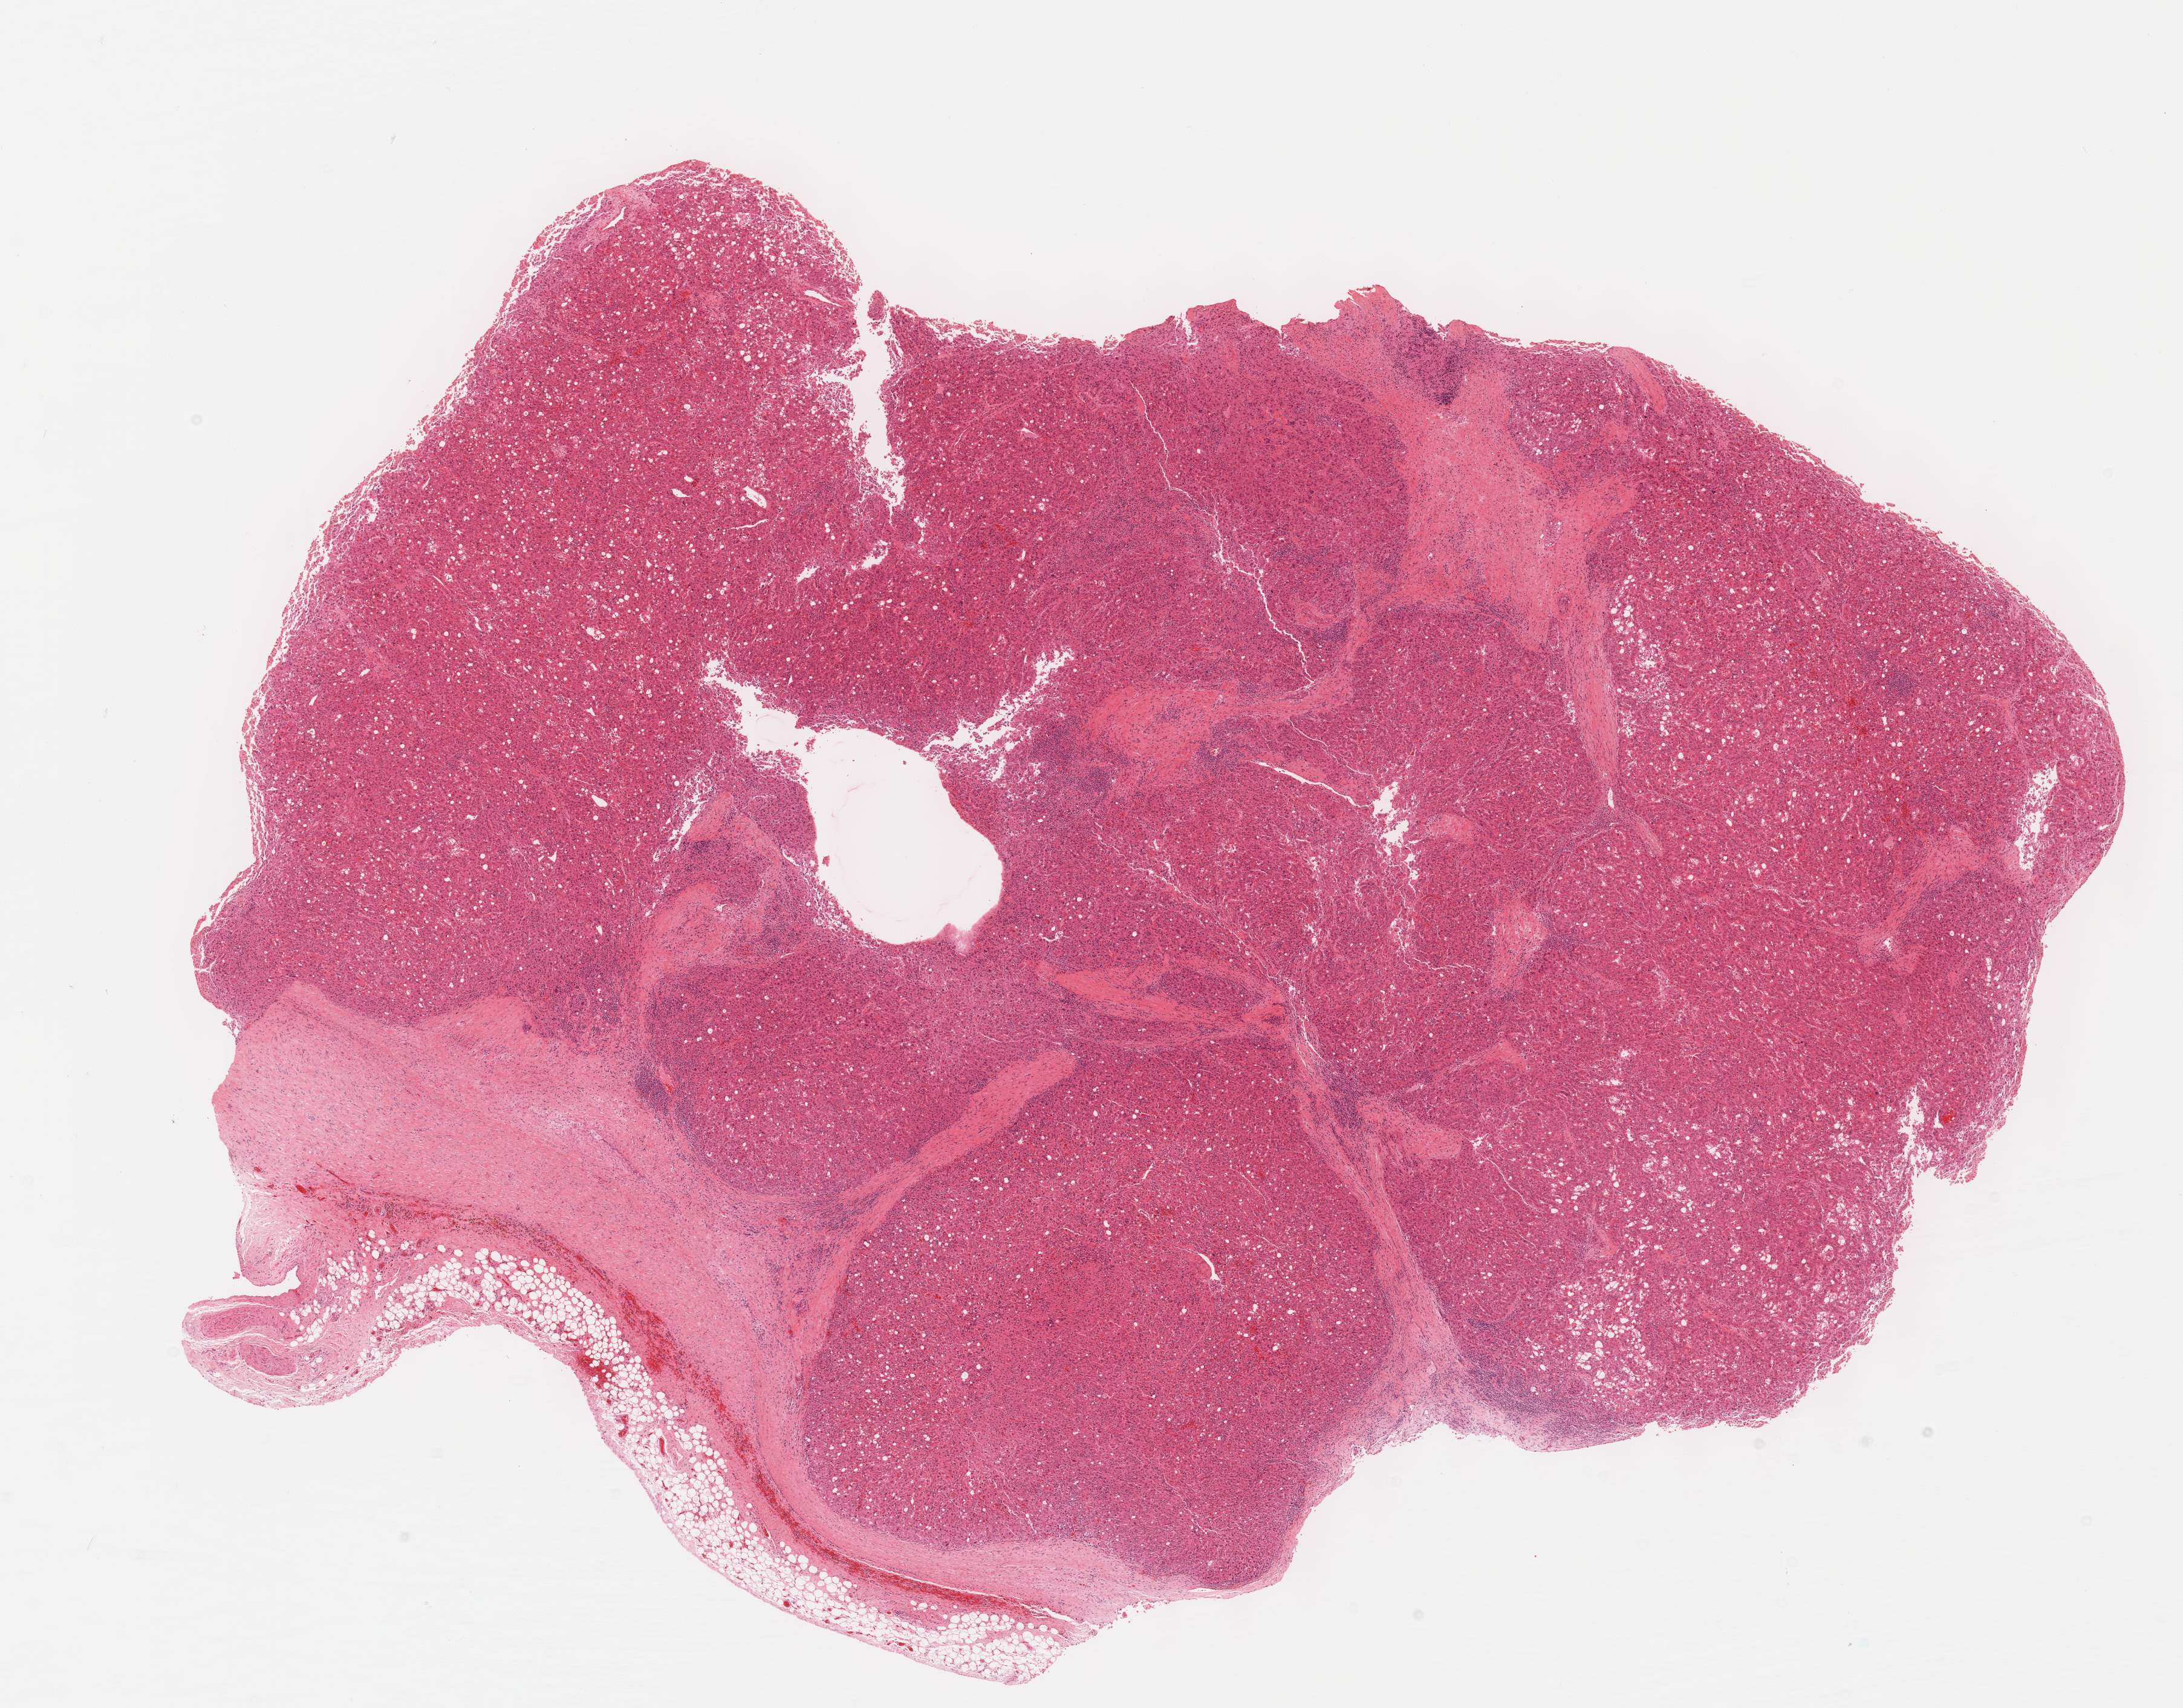
H&E-stained whole-slide image, a low-resolution overview of the entire scanned area, about 14.6 x 11.4 mm; formalin-fixed paraffin-embedded (FFPE) diagnostic section; sample: primary tumour, liver. Male, age 69 years at initial diagnosis. Histologic grade: G3 (poorly differentiated).
- AJCC pathologic stage: II (6th edition)
- histologic diagnosis: Hepatocellular carcinoma, NOS